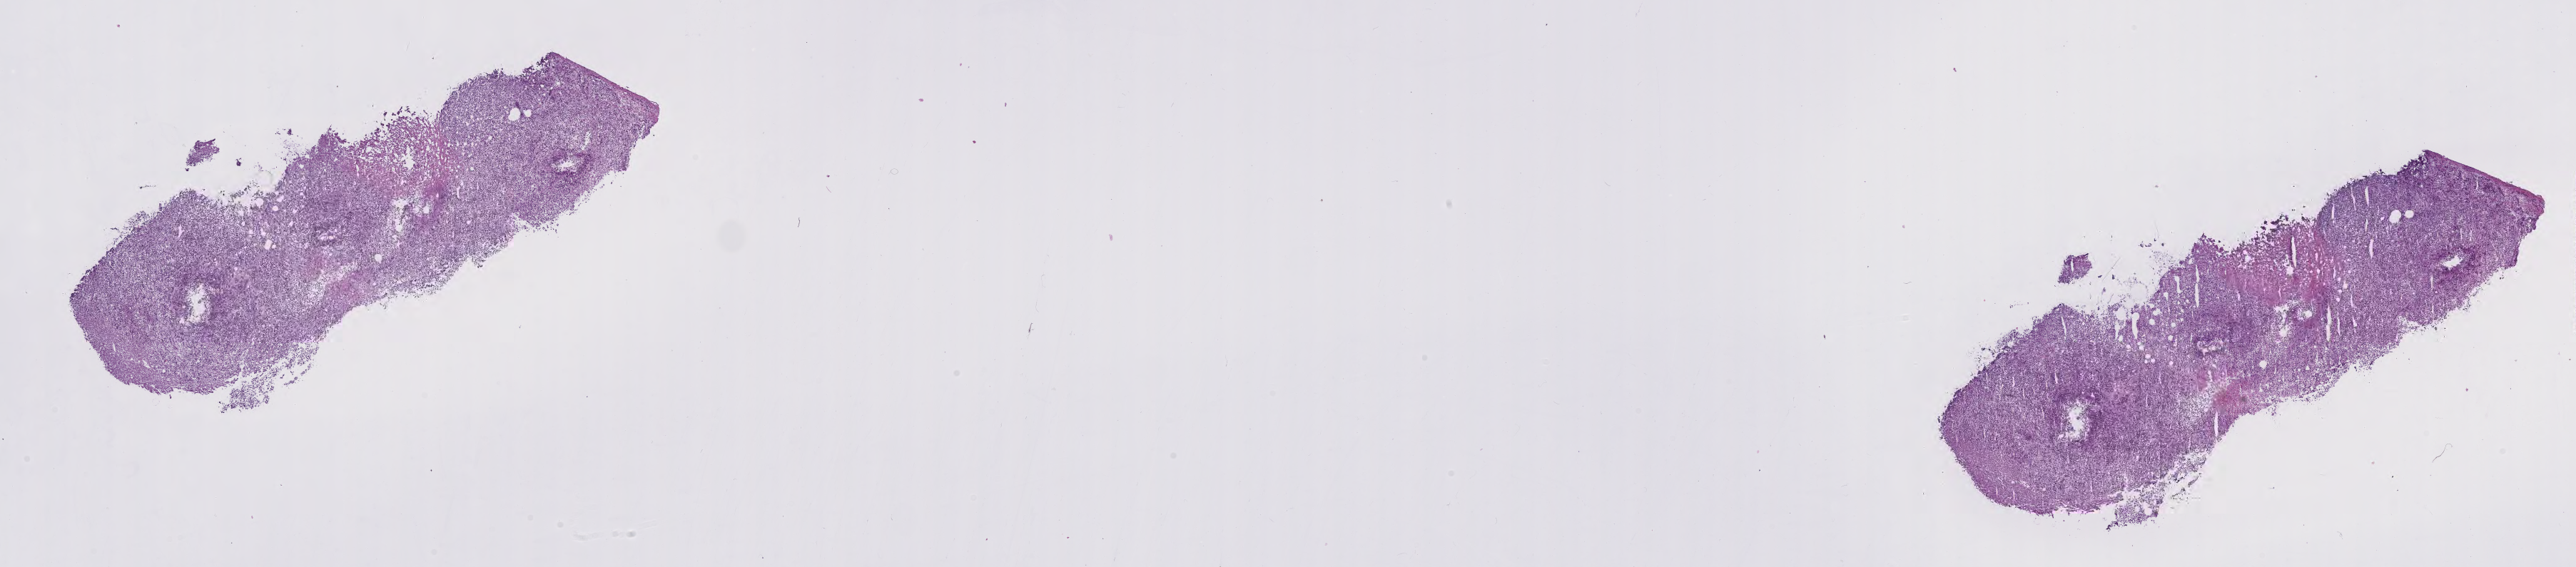
Whole-slide image, hematoxylin and eosin (H&E) stain of tumor tissue from the adrenal gland, a low-resolution overview of the entire scanned area, about 29.2 x 6.4 mm; cryosection (OCT / tissue freezing medium). Patient: male, age 51 months.
Diagnosis (ICD-O-3 morphology term): Sarcoma, NOS.